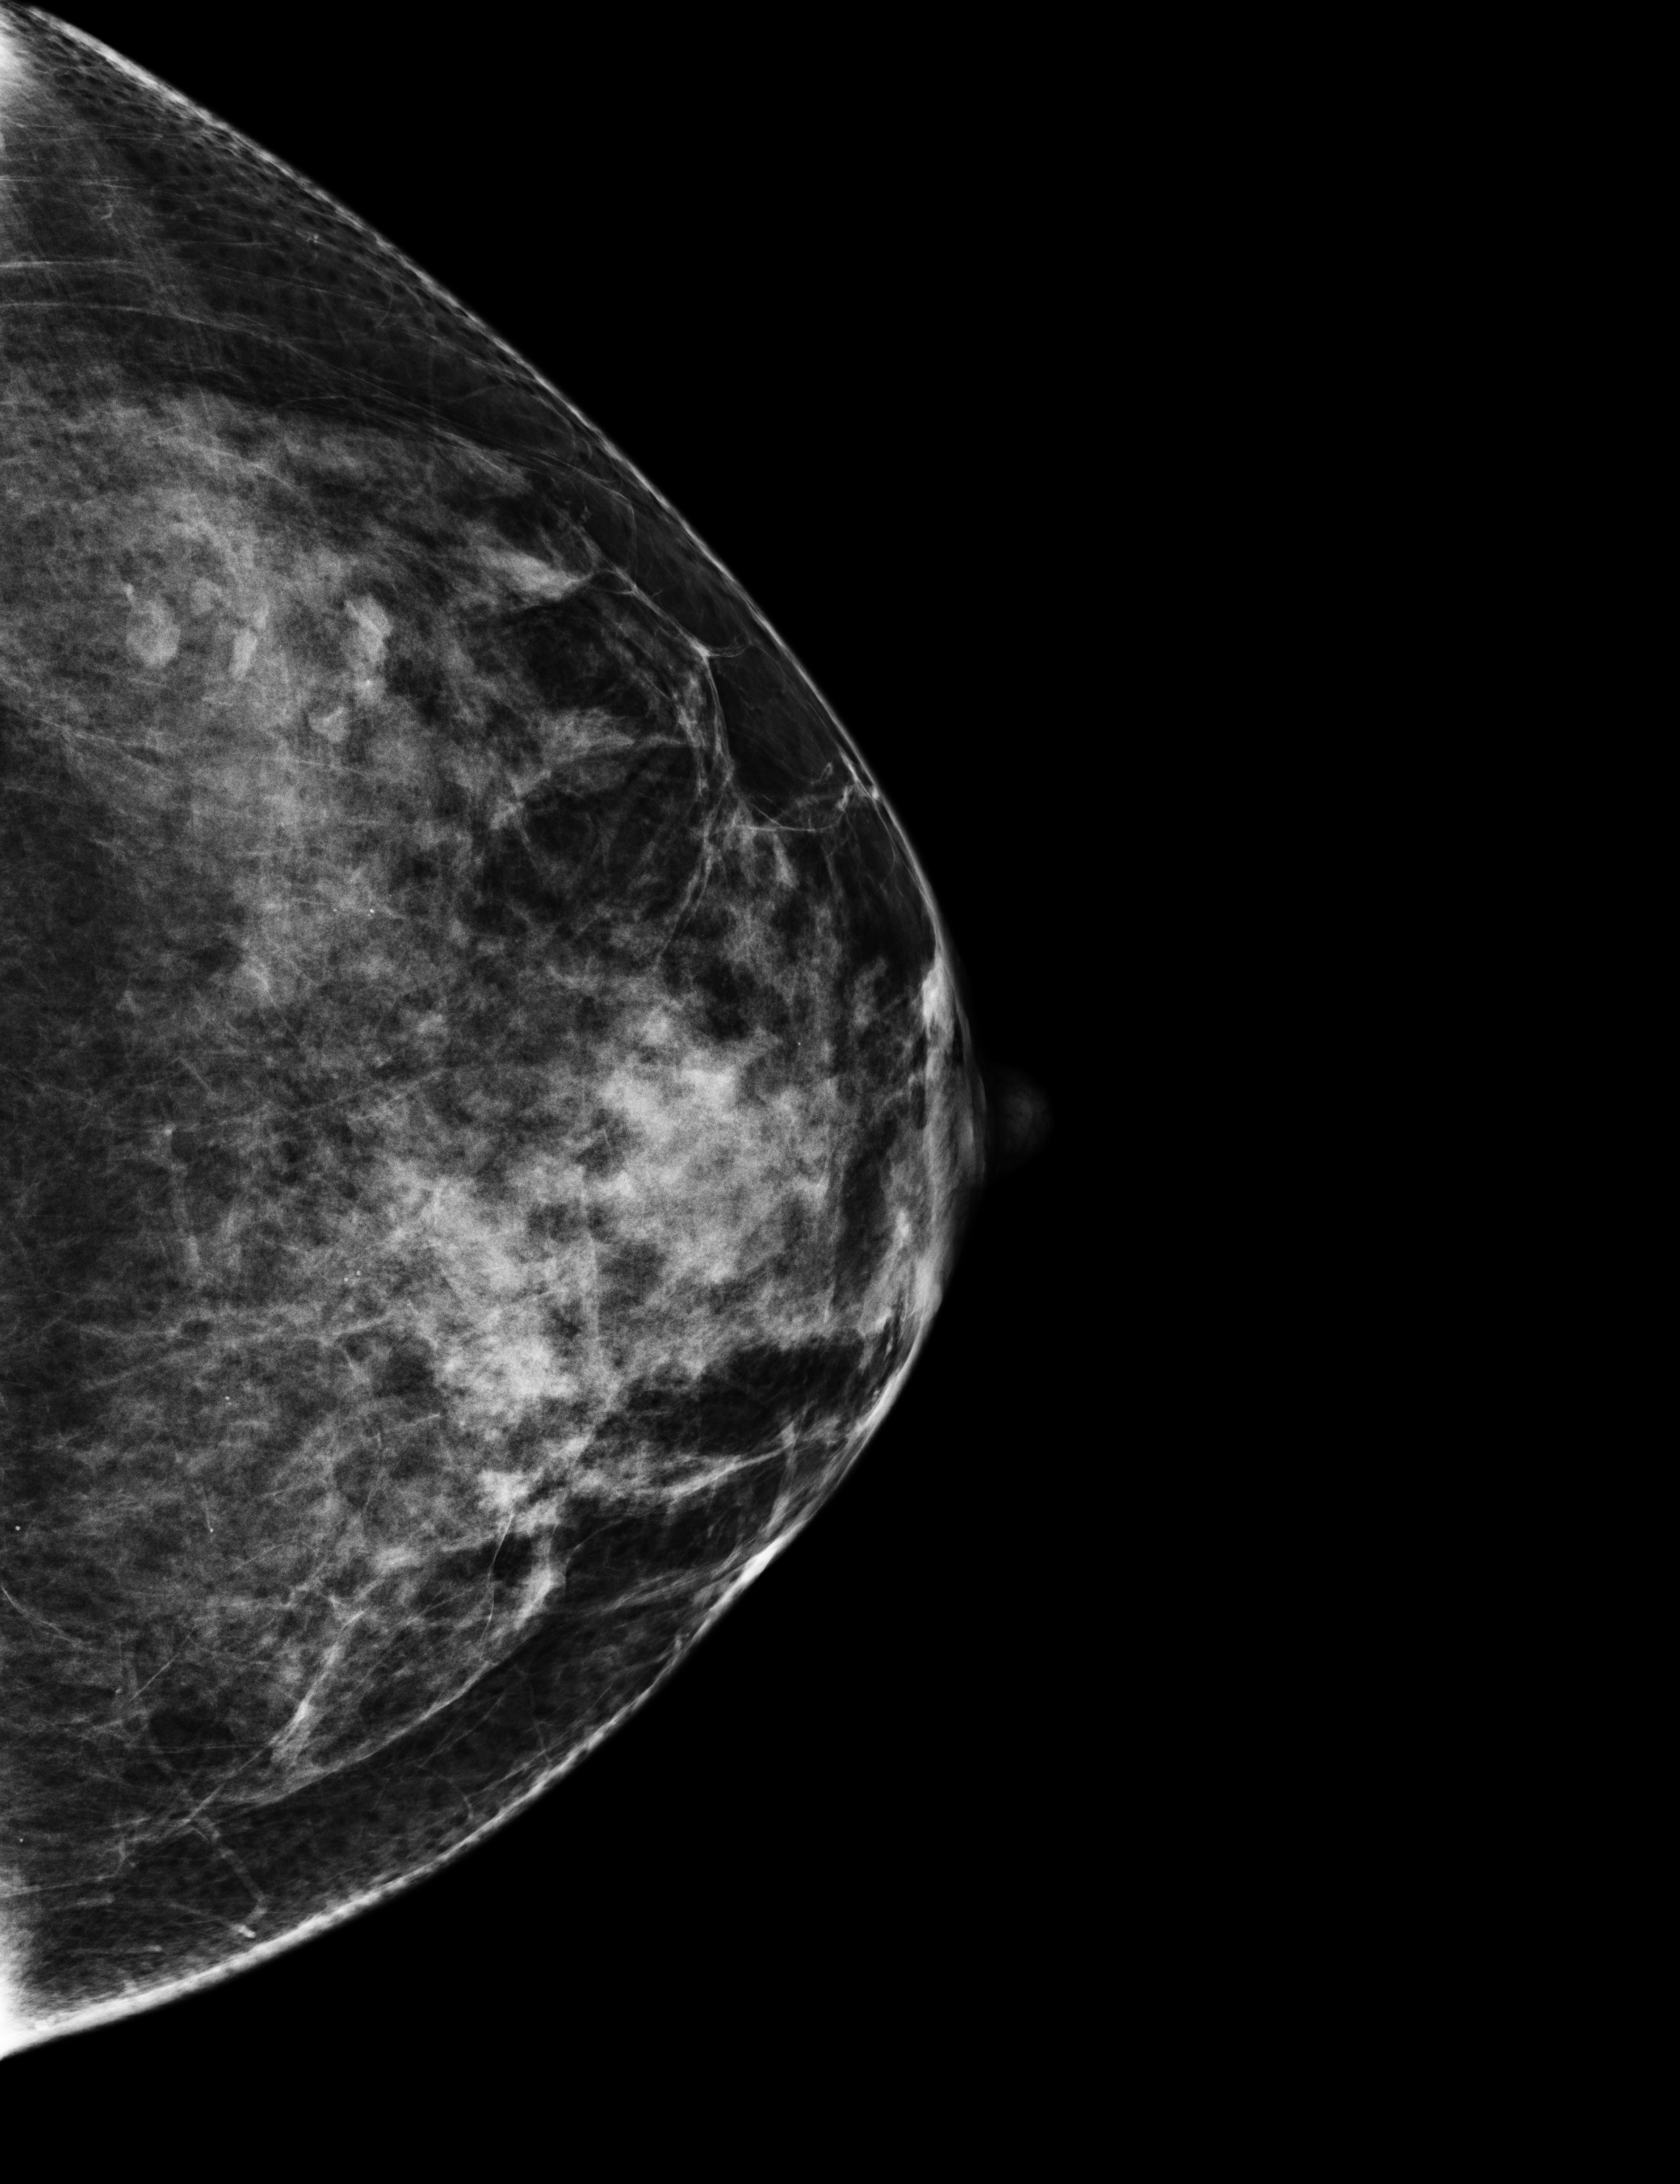
Screening examination, compressed breast thickness 67 mm. Female patient, age 47 years.
Image type: full-field digital mammogram. Breast: left. Projection: cranio-caudal projection.